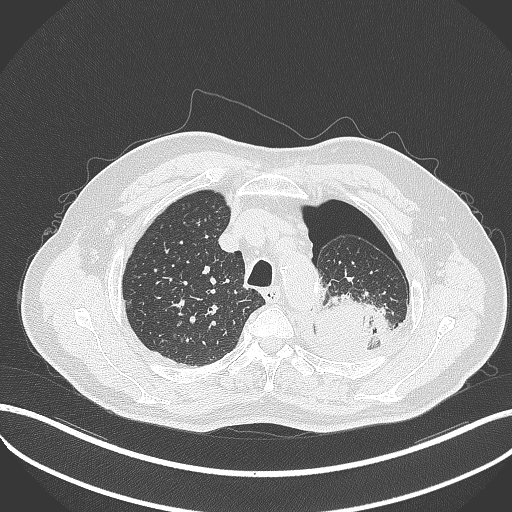
Chest CT, one axial slice; reconstruction kernel B70f; 120 kVp; lung window (W 1500 / L -600 HU); 1 mm slice thickness; 512 × 512 image matrix. Patient: male, 76 years. Case-level facts recorded for this patient, not image findings: clinical TNM (as recorded): T3 N0 M1b.
Structures marked on this image (rectangle marked by the reading radiologist):
- lung tumour (recorded histology: adenocarcinoma): box from (x=312, y=286) to (x=392, y=349) px